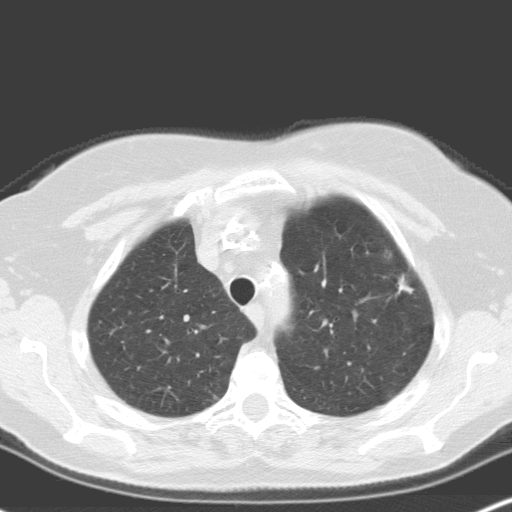
Low-dose screening chest CT, one axial slice. Slice 134 of 160 in the series (ordered by position). 120 kVp. Lung window (W 1500 / L -600 HU). 3.2 mm slice thickness. 512 × 512 image matrix.
Outlined on this slice (manually delineated by an expert):
- lesion 2 (nodule): bounding box <399,276,410,291> (left, top, right, bottom; pixels)